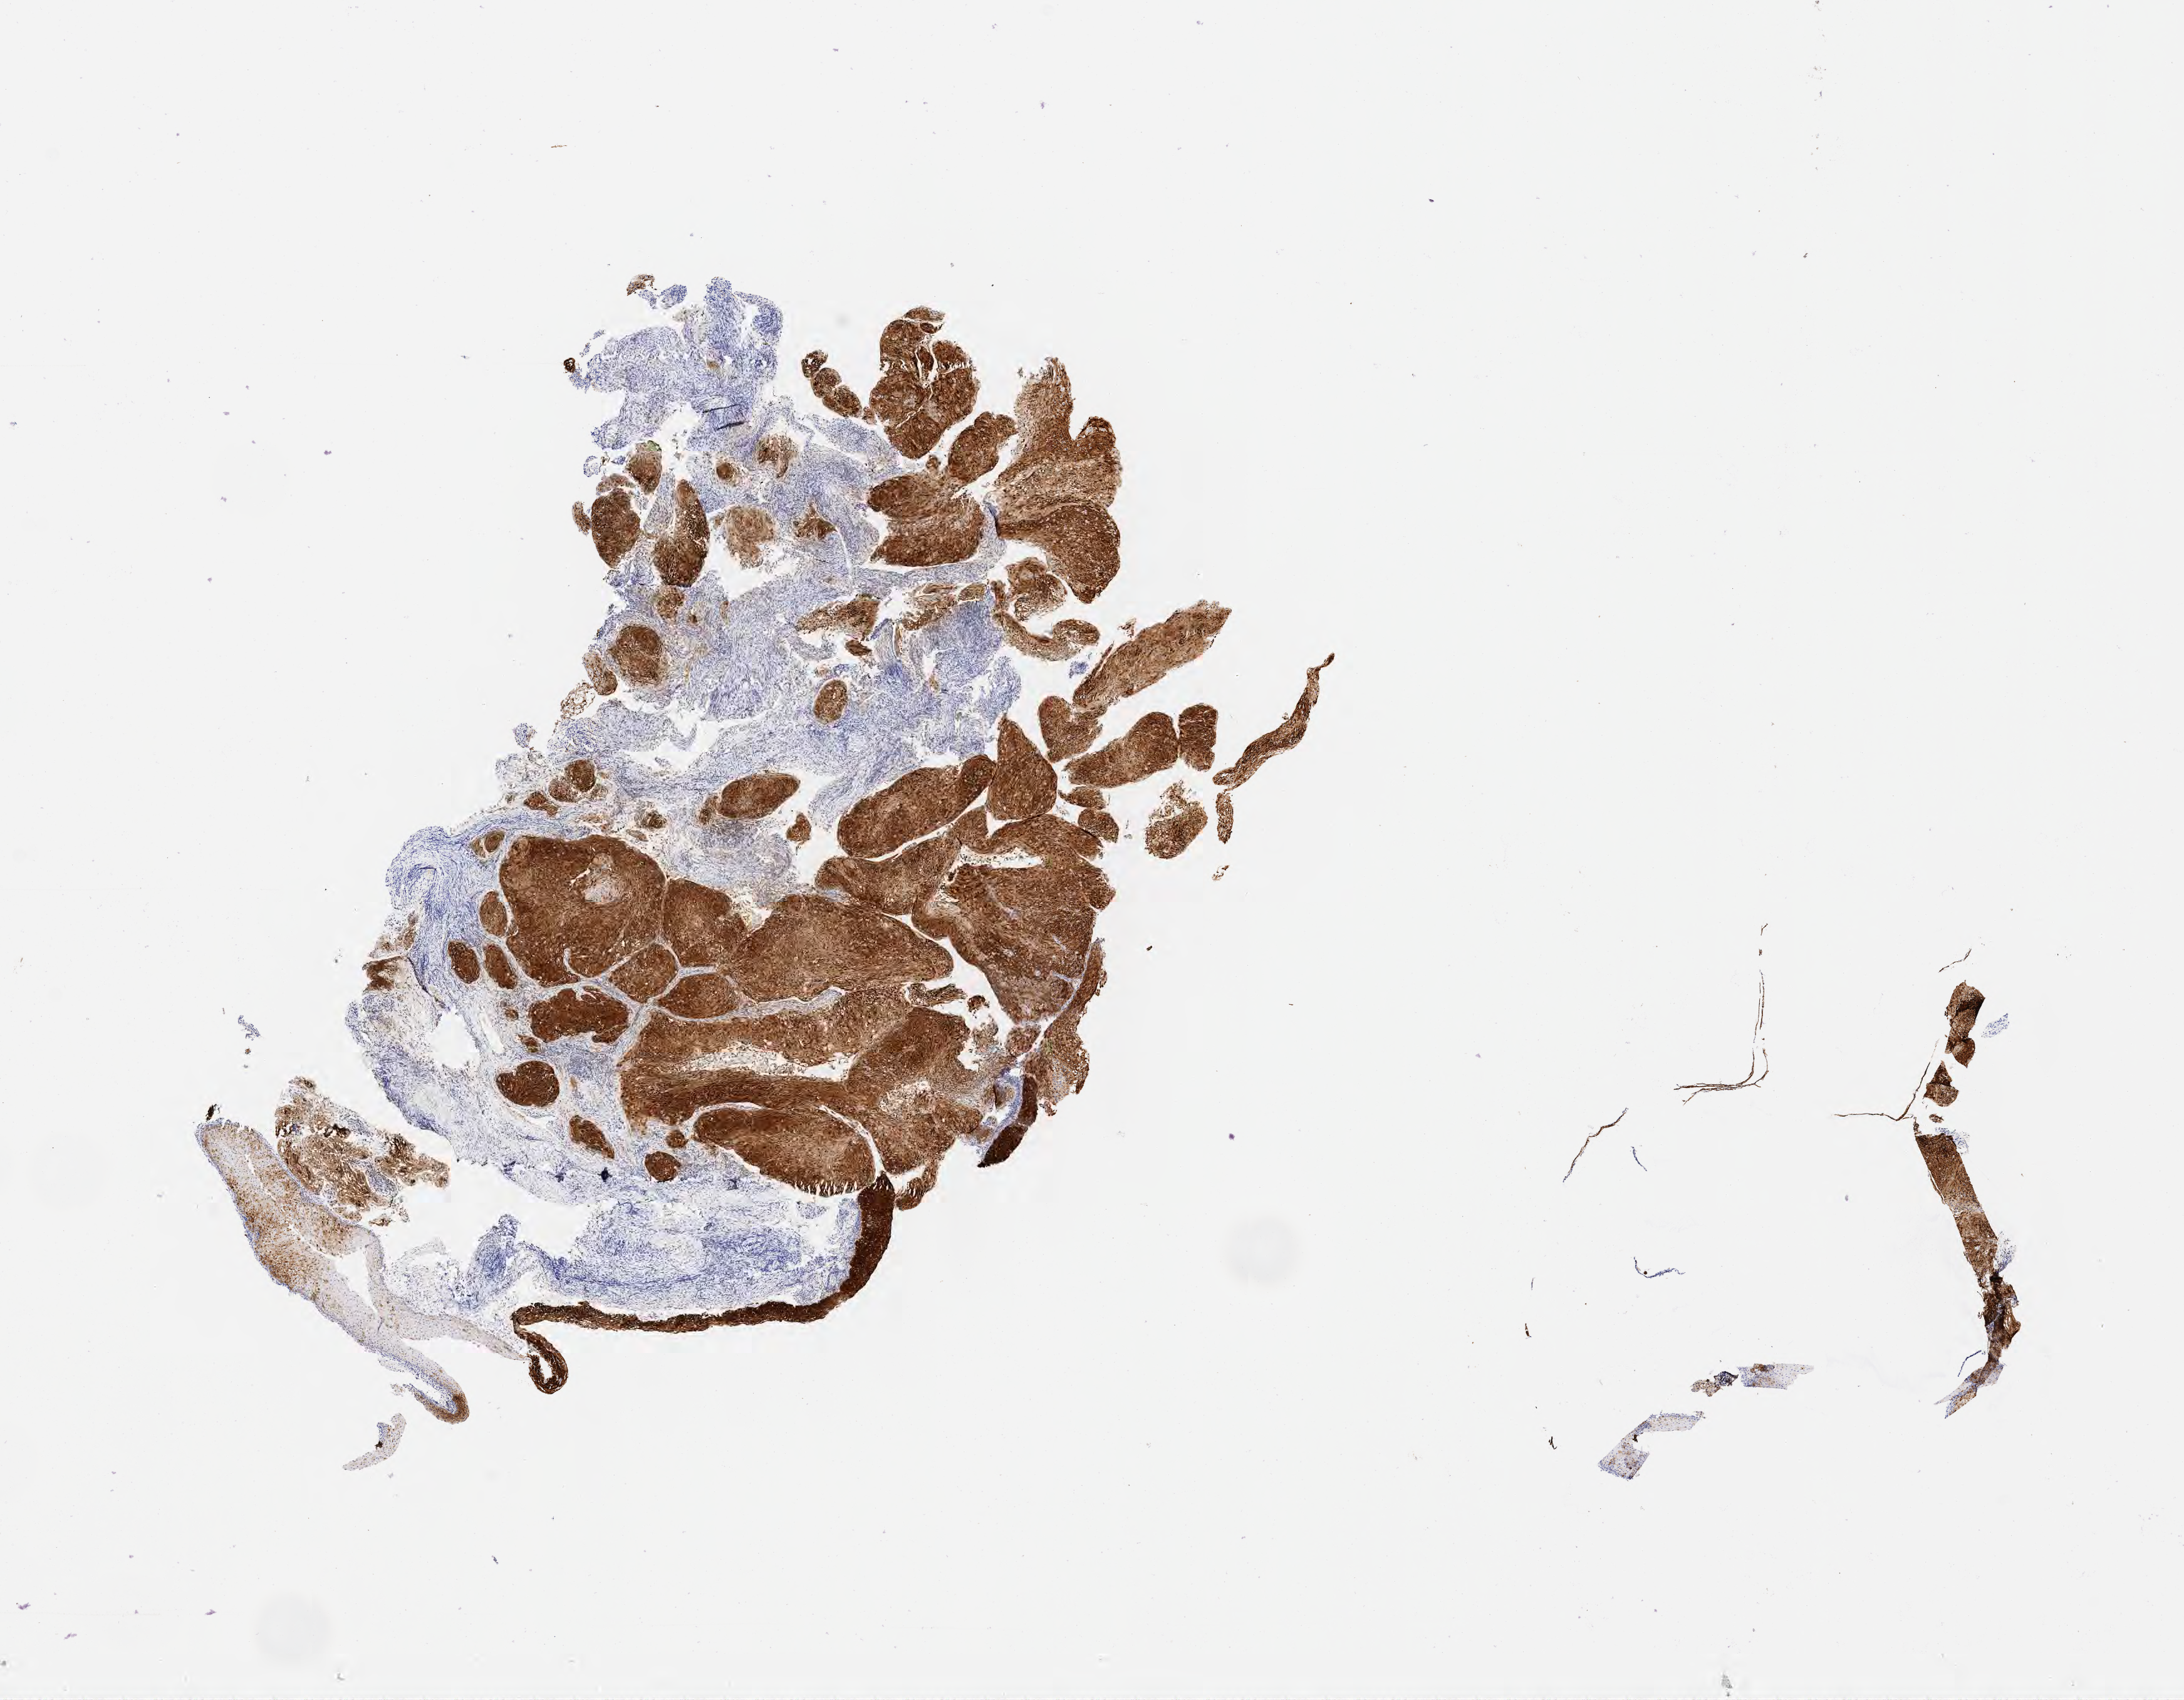
IHC for p16 (p16INK4a), whole-slide image — a low-resolution overview of the entire scanned area, about 14.1 x 11.0 mm, tumor tissue, site: cervix. Patient female; age 82 years.
- histologic diagnosis: Squamous cell carcinoma, large cell, nonkeratinizing, NOS